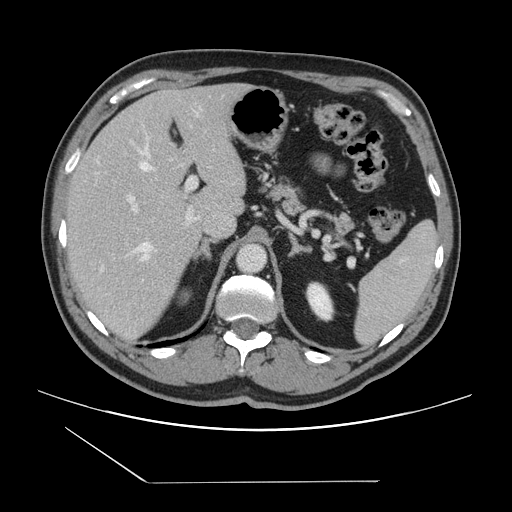
Contrast-enhanced abdominal CT, one axial slice; 120 kVp; intravenous contrast given; soft-tissue window (W 400 / L 40 HU); 2.5 mm slice thickness; 512 × 512 image matrix, field of view 407 × 407 mm. Male patient, age 61 years. Case-level facts recorded for this patient, not image findings: diagnosis: colorectal cancer liver metastases, imaged before liver resection.
Outlined on this slice (expert manual segmentation):
- hepatic veins: box from (x=102, y=114) to (x=199, y=269) px
- liver: (x=65, y=84)–(x=246, y=340)
- planned liver remnant (the part of the liver to remain after resection): (x=67, y=84)–(x=238, y=223)
- portal vein (with intrahepatic branches): (x=127, y=176)–(x=199, y=223)